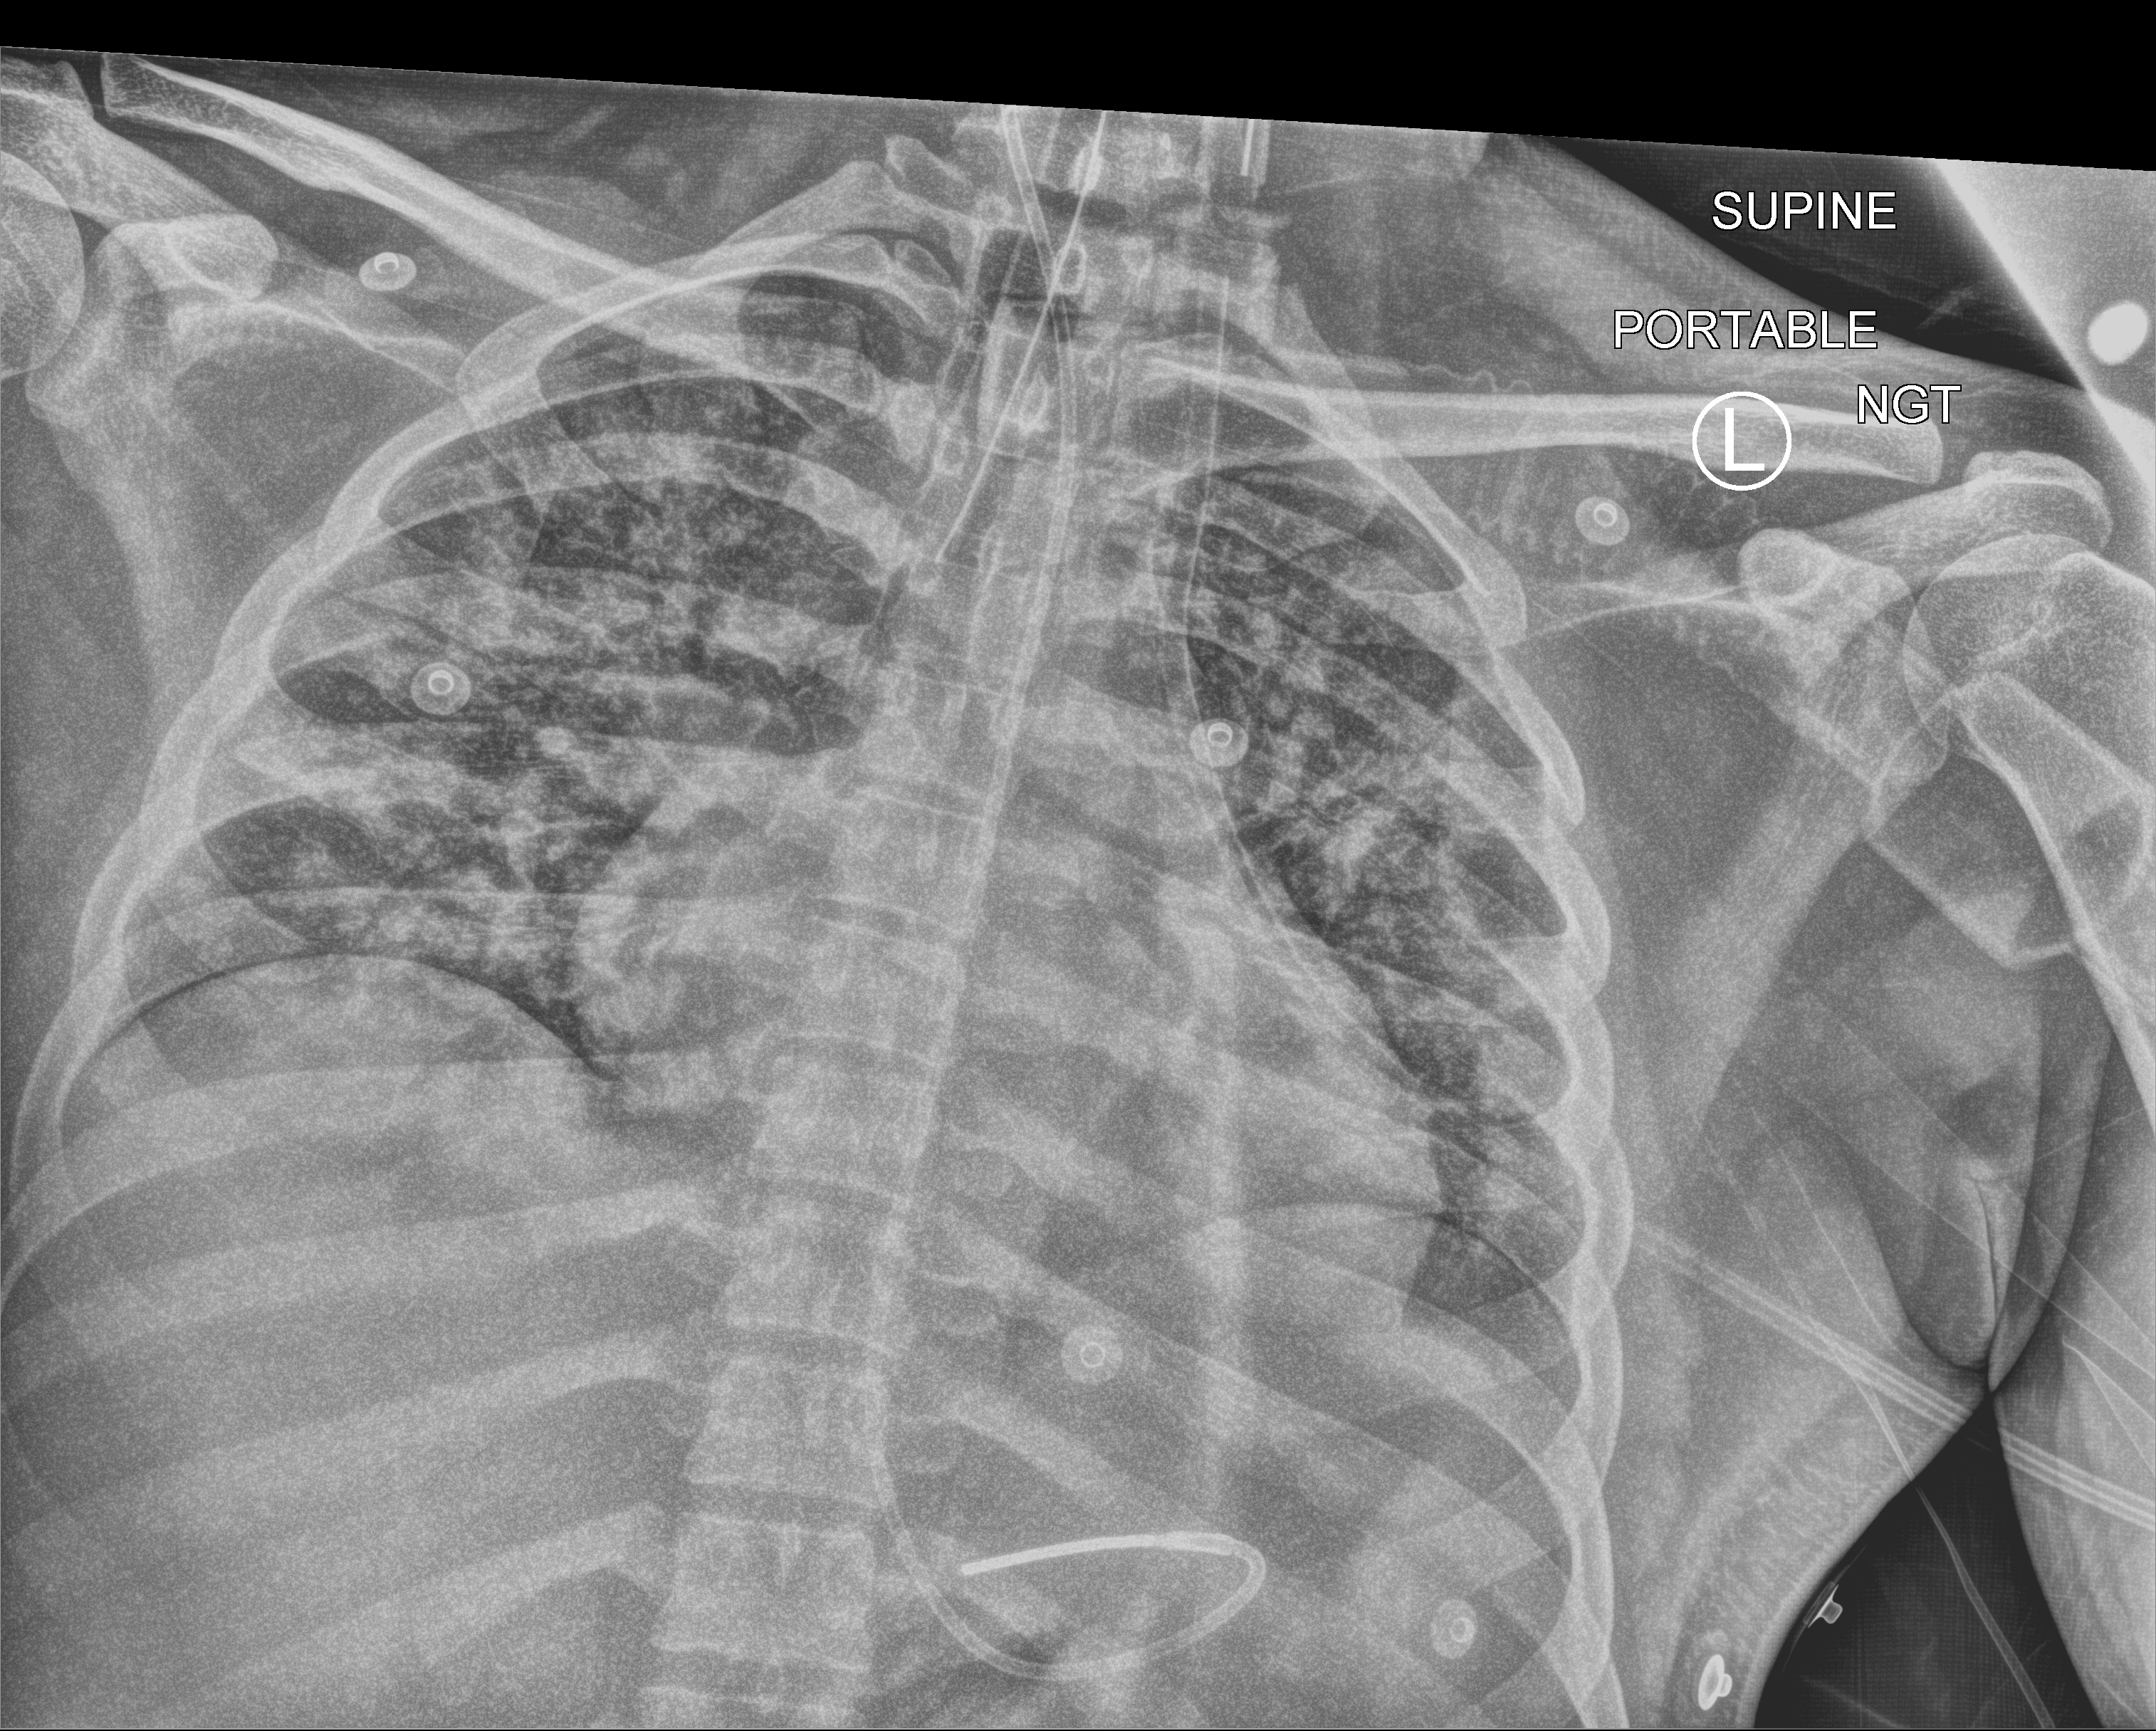
Bedside chest radiograph (computed radiography); anteroposterior (AP) projection. Male patient hospitalised with COVID-19, age 18–59 years.
Hospital-stay facts (about this admission, not read from this image; timing relative to this image not recorded): length of hospital stay: 16 days; mechanically ventilated during this hospital stay: yes.